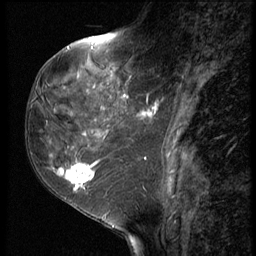
Breast MRI (dynamic contrast-enhanced), one sagittal slice. Slice 26 of 62 in the series (ordered by position). 3 images stored at this slice position (order not interpretable as contrast timing). 1.5 T. TE 4.2 ms, TR 9 ms. 2.5 mm slice thickness. 256 × 256 image matrix. Female patient, age 50 years. Case-level facts recorded for this patient, not image findings: setting: breast cancer imaged before/during neoadjuvant chemotherapy; receptor status: HR-positive, HER2-negative.
Outlined on this slice (semi-automatically segmented with operator editing):
- analysis volume of interest (the breast-tissue region the enhancement analysis was run in; not a lesion): bounding box (x1, y1, x2, y2) in pixels: (32, 91, 118, 209)
- tumour enhancement mask (voxels above the 140 % enhancement threshold inside the analysis volume of interest): (59, 164, 94, 190)